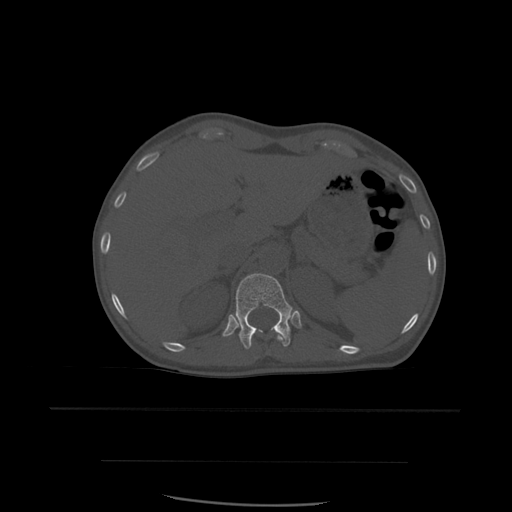
CT including the spine, one axial slice; position 278 of 574 along the scan axis; bone window (W 1800 / L 400 HU); 1.25 mm slice thickness; 512 × 512 image matrix. Patient age 48 years. From the clinical record (not read from this slice): primary cancer: lung.
Outlined on this slice (semi-automatically segmented with operator editing):
- T11 vertebra: bounding box <251,333,284,346> (left, top, right, bottom; pixels)
- T12 vertebra: <236,274,293,350>